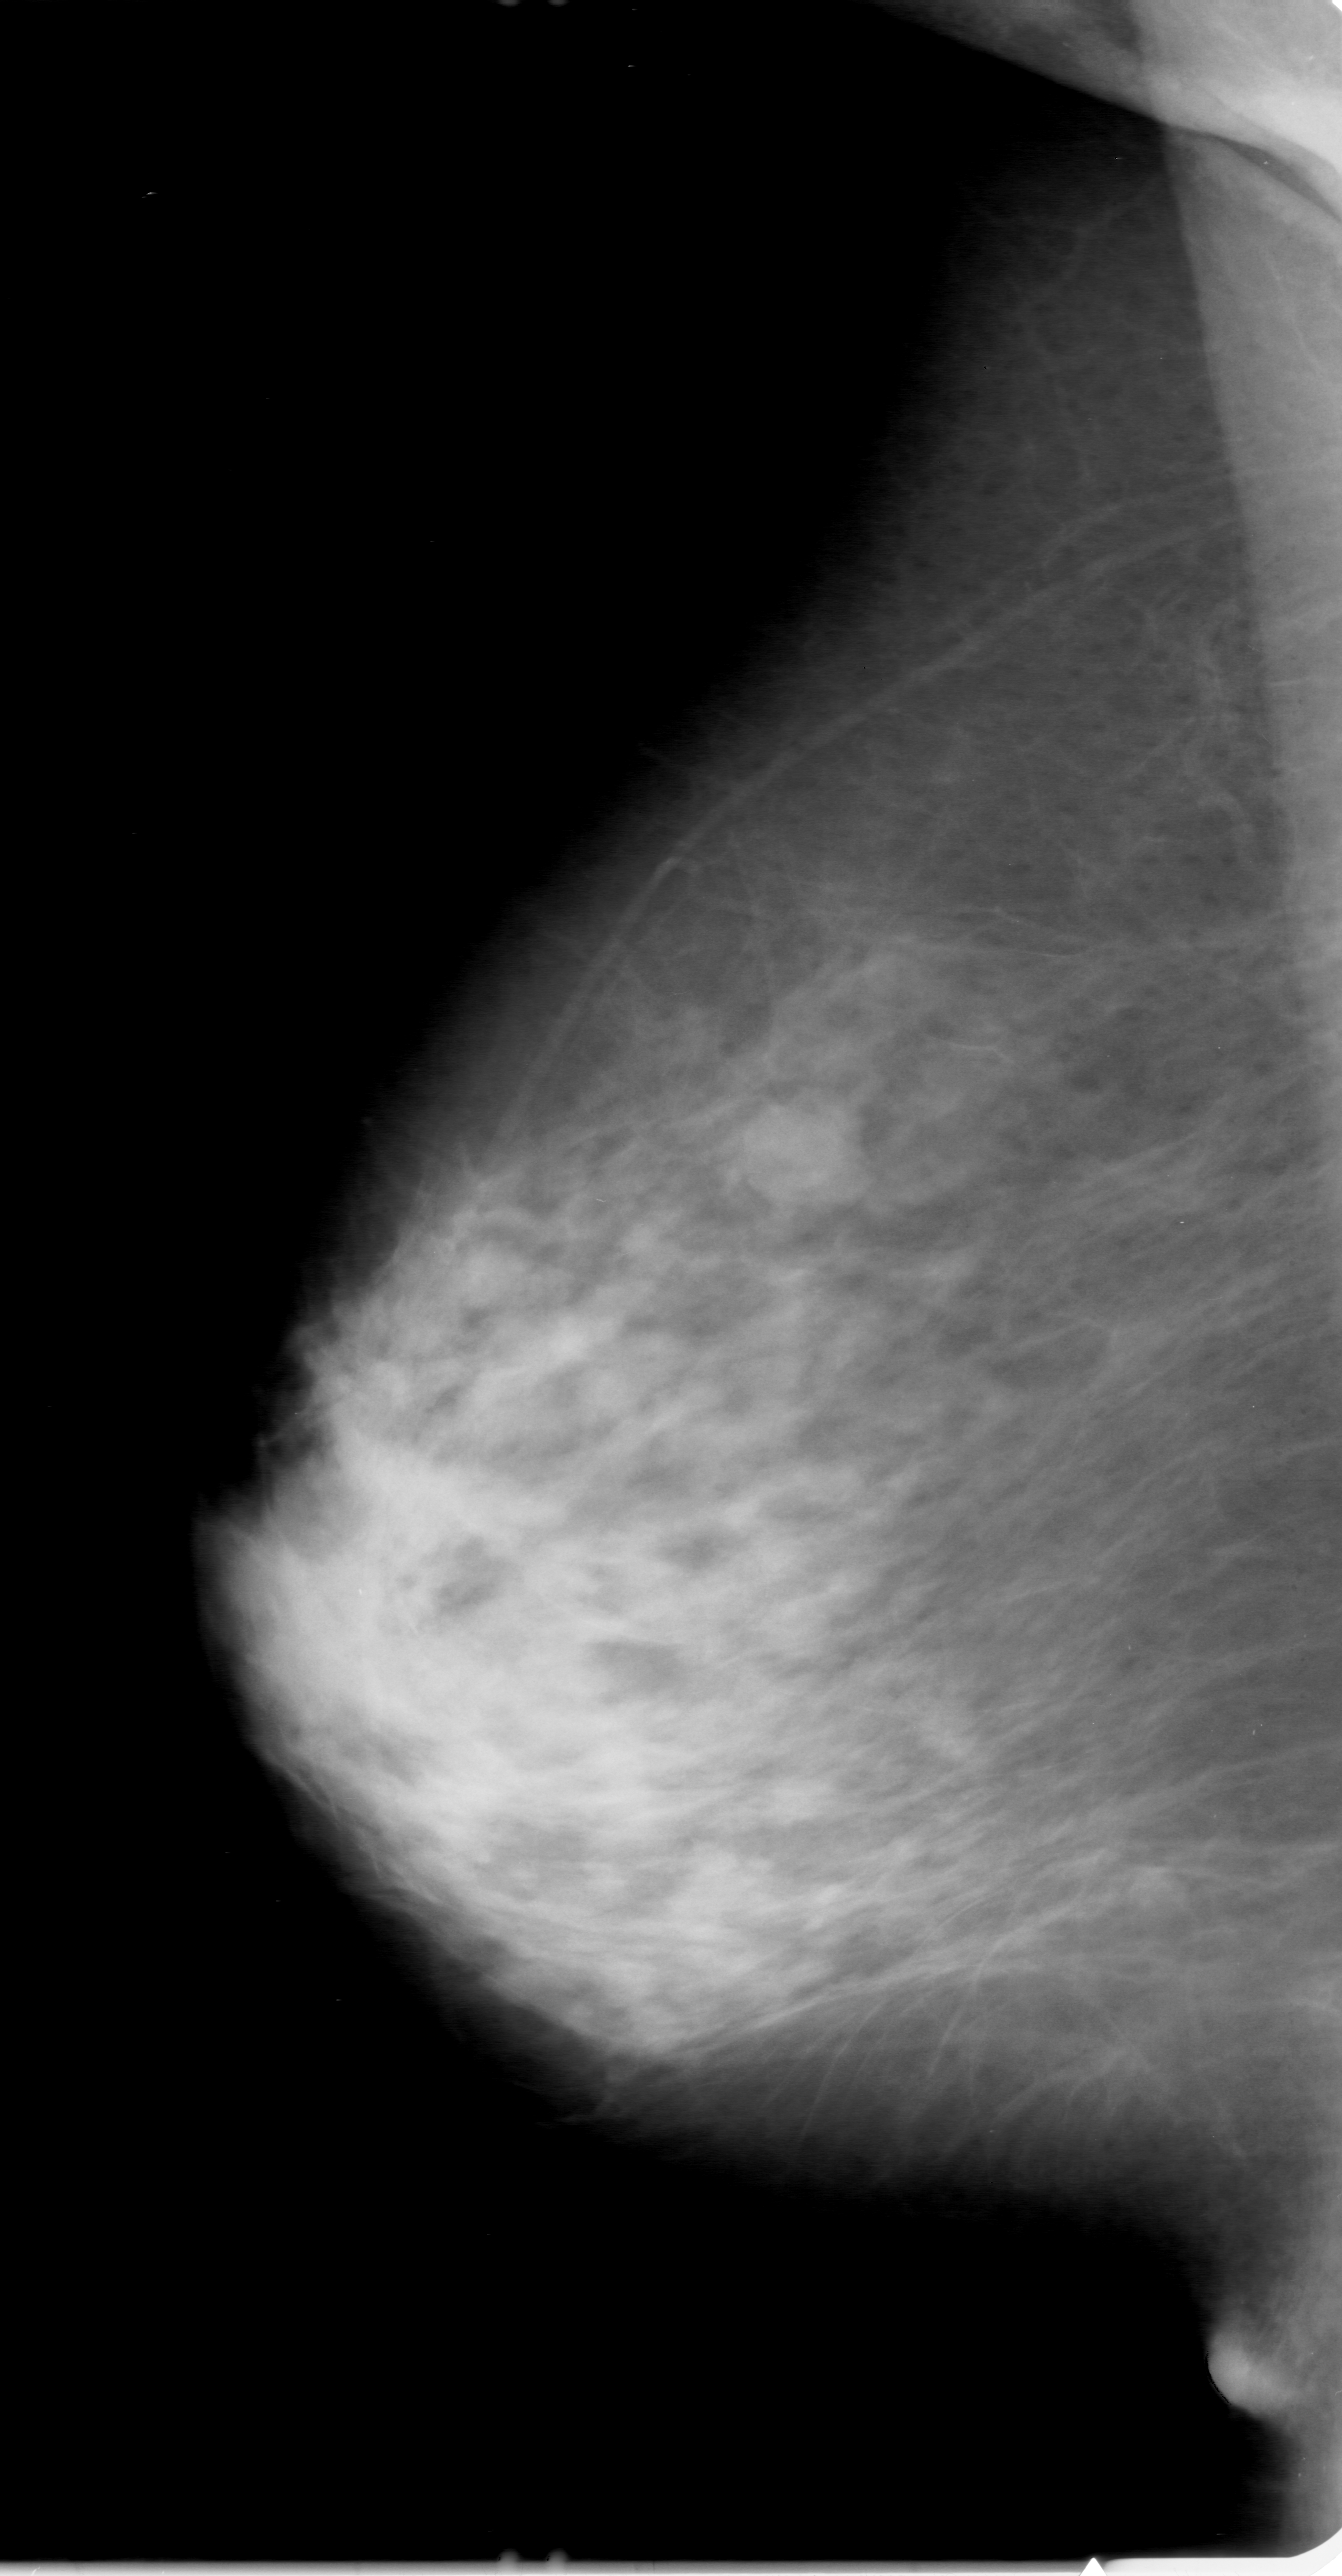
Scanned film-screen mammogram; right breast; mediolateral oblique (MLO) view; breast composition: heterogeneously dense (BI-RADS density category 3 of 4).
Mass, shape lobulated, margins circumscribed; BI-RADS assessment category 0 (incomplete: needs additional imaging); pathology (as recorded): malignant.